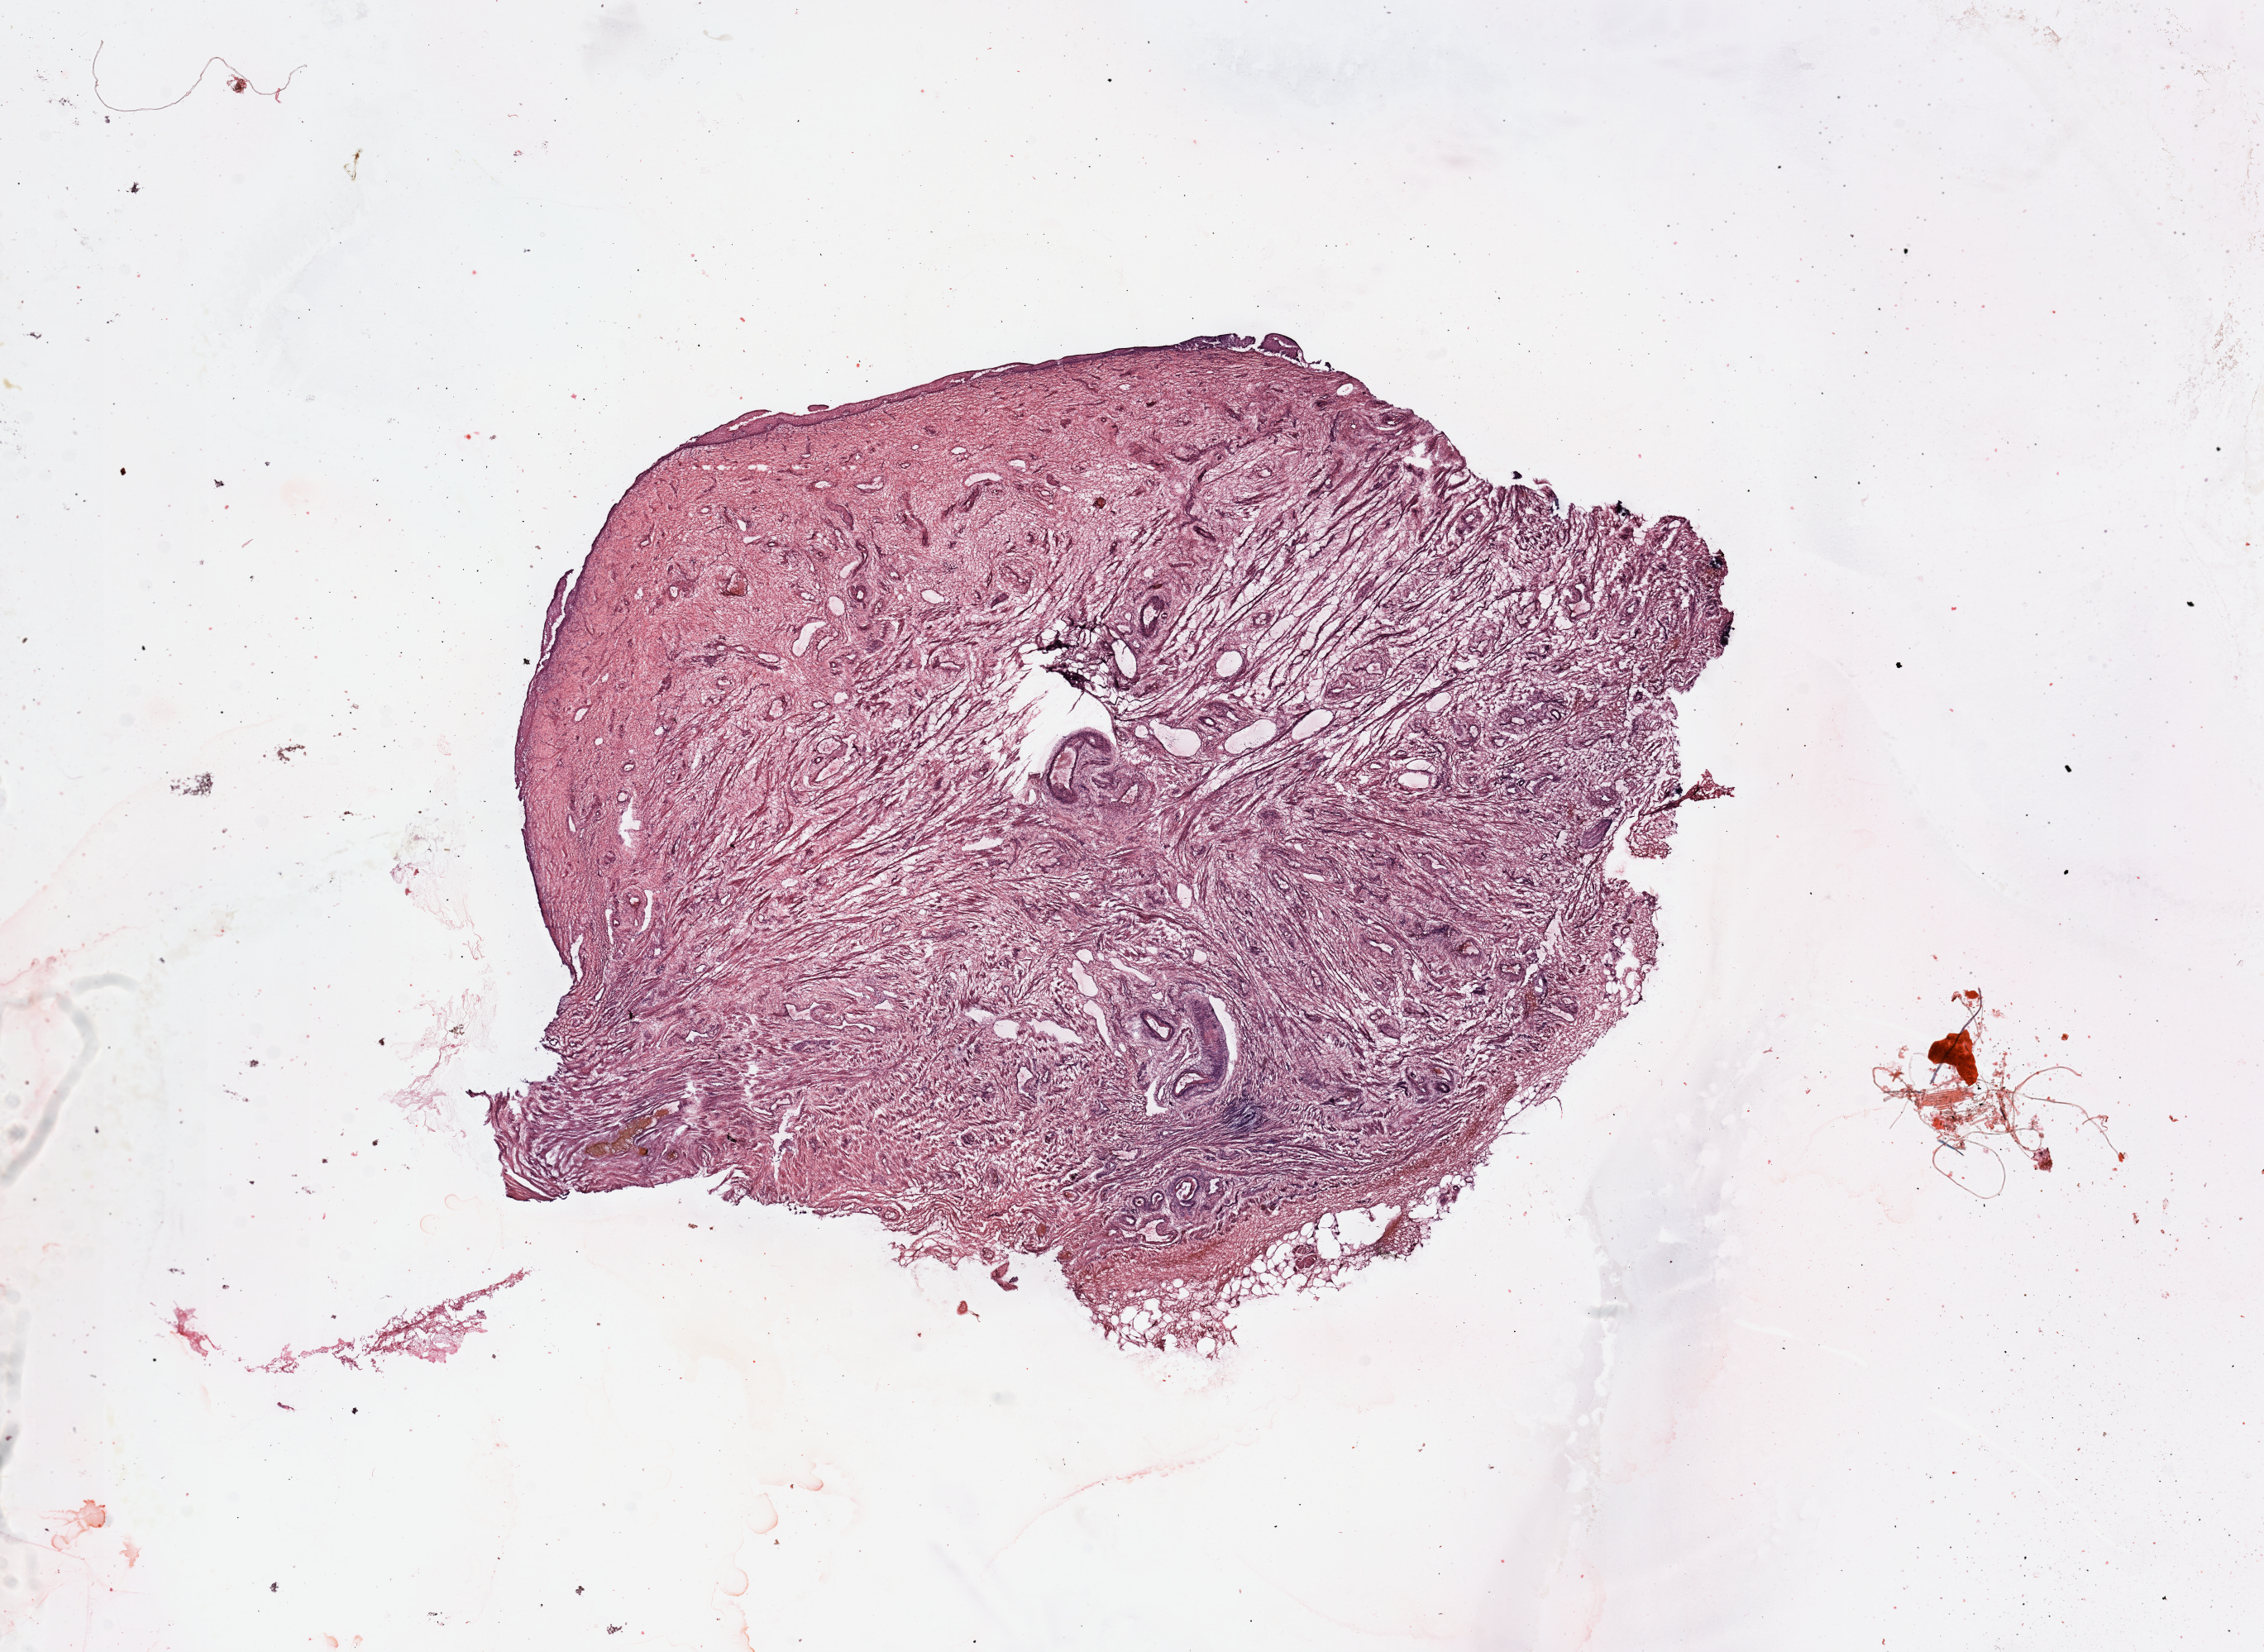
Digitized H&E tissue section (whole slide) — shown as a low-resolution overview of the whole scanned area (about 21.7 x 15.8 mm, slide scanned at 20x), uterus, normal (non-tumour) tissue. 59-year-old female patient.
This section: normal (non-tumour) tissue from the same patient. Patient diagnosis: Endometrioid adenocarcinoma, NOS.